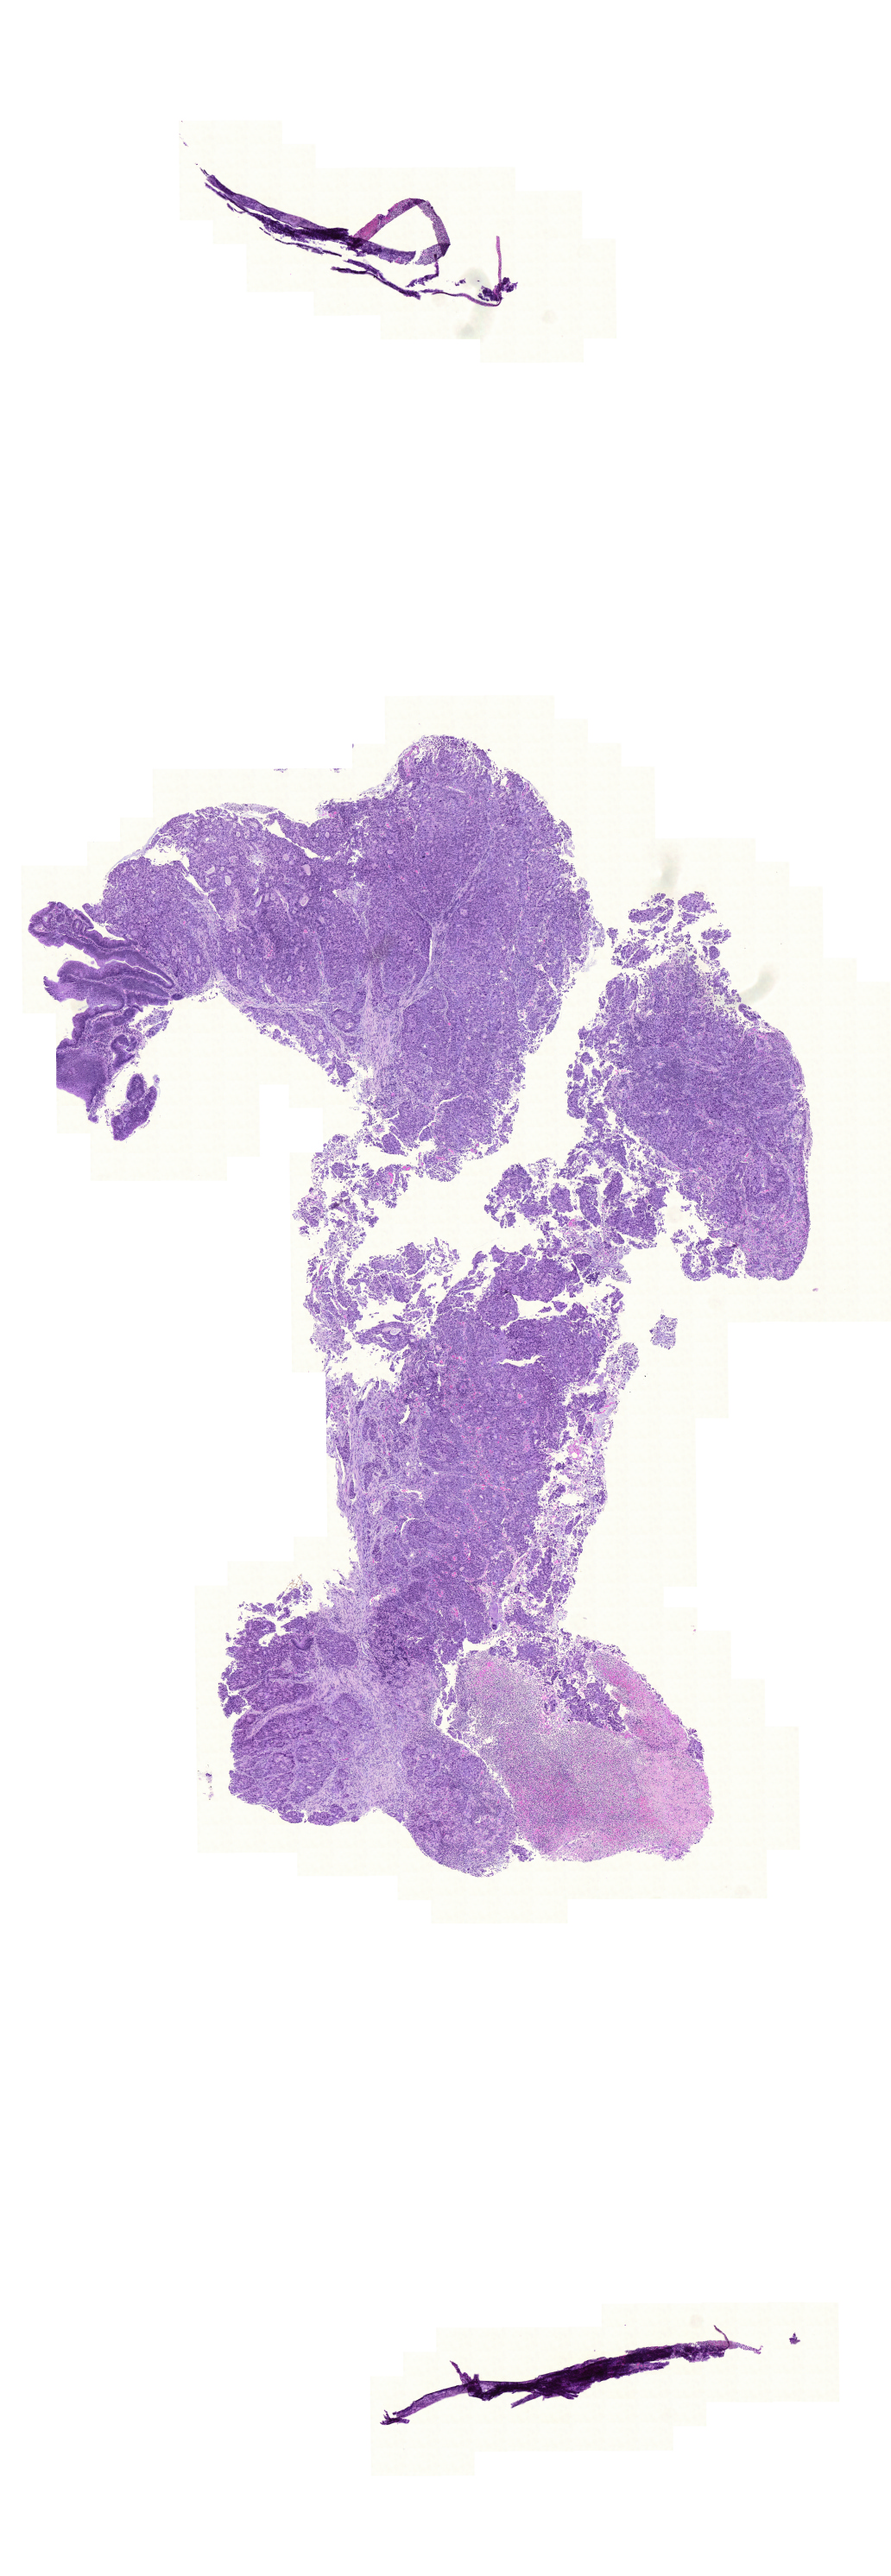
Hematoxylin and eosin (H&E) stained whole-slide image, low-resolution overview of the scanned area, about 7.7 x 22.2 mm, formalin-fixed paraffin-embedded (FFPE) diagnostic section, primary tumour sample from the rectum. Male, age 80 years at initial diagnosis.
Pathologic diagnosis: Adenocarcinoma, NOS.